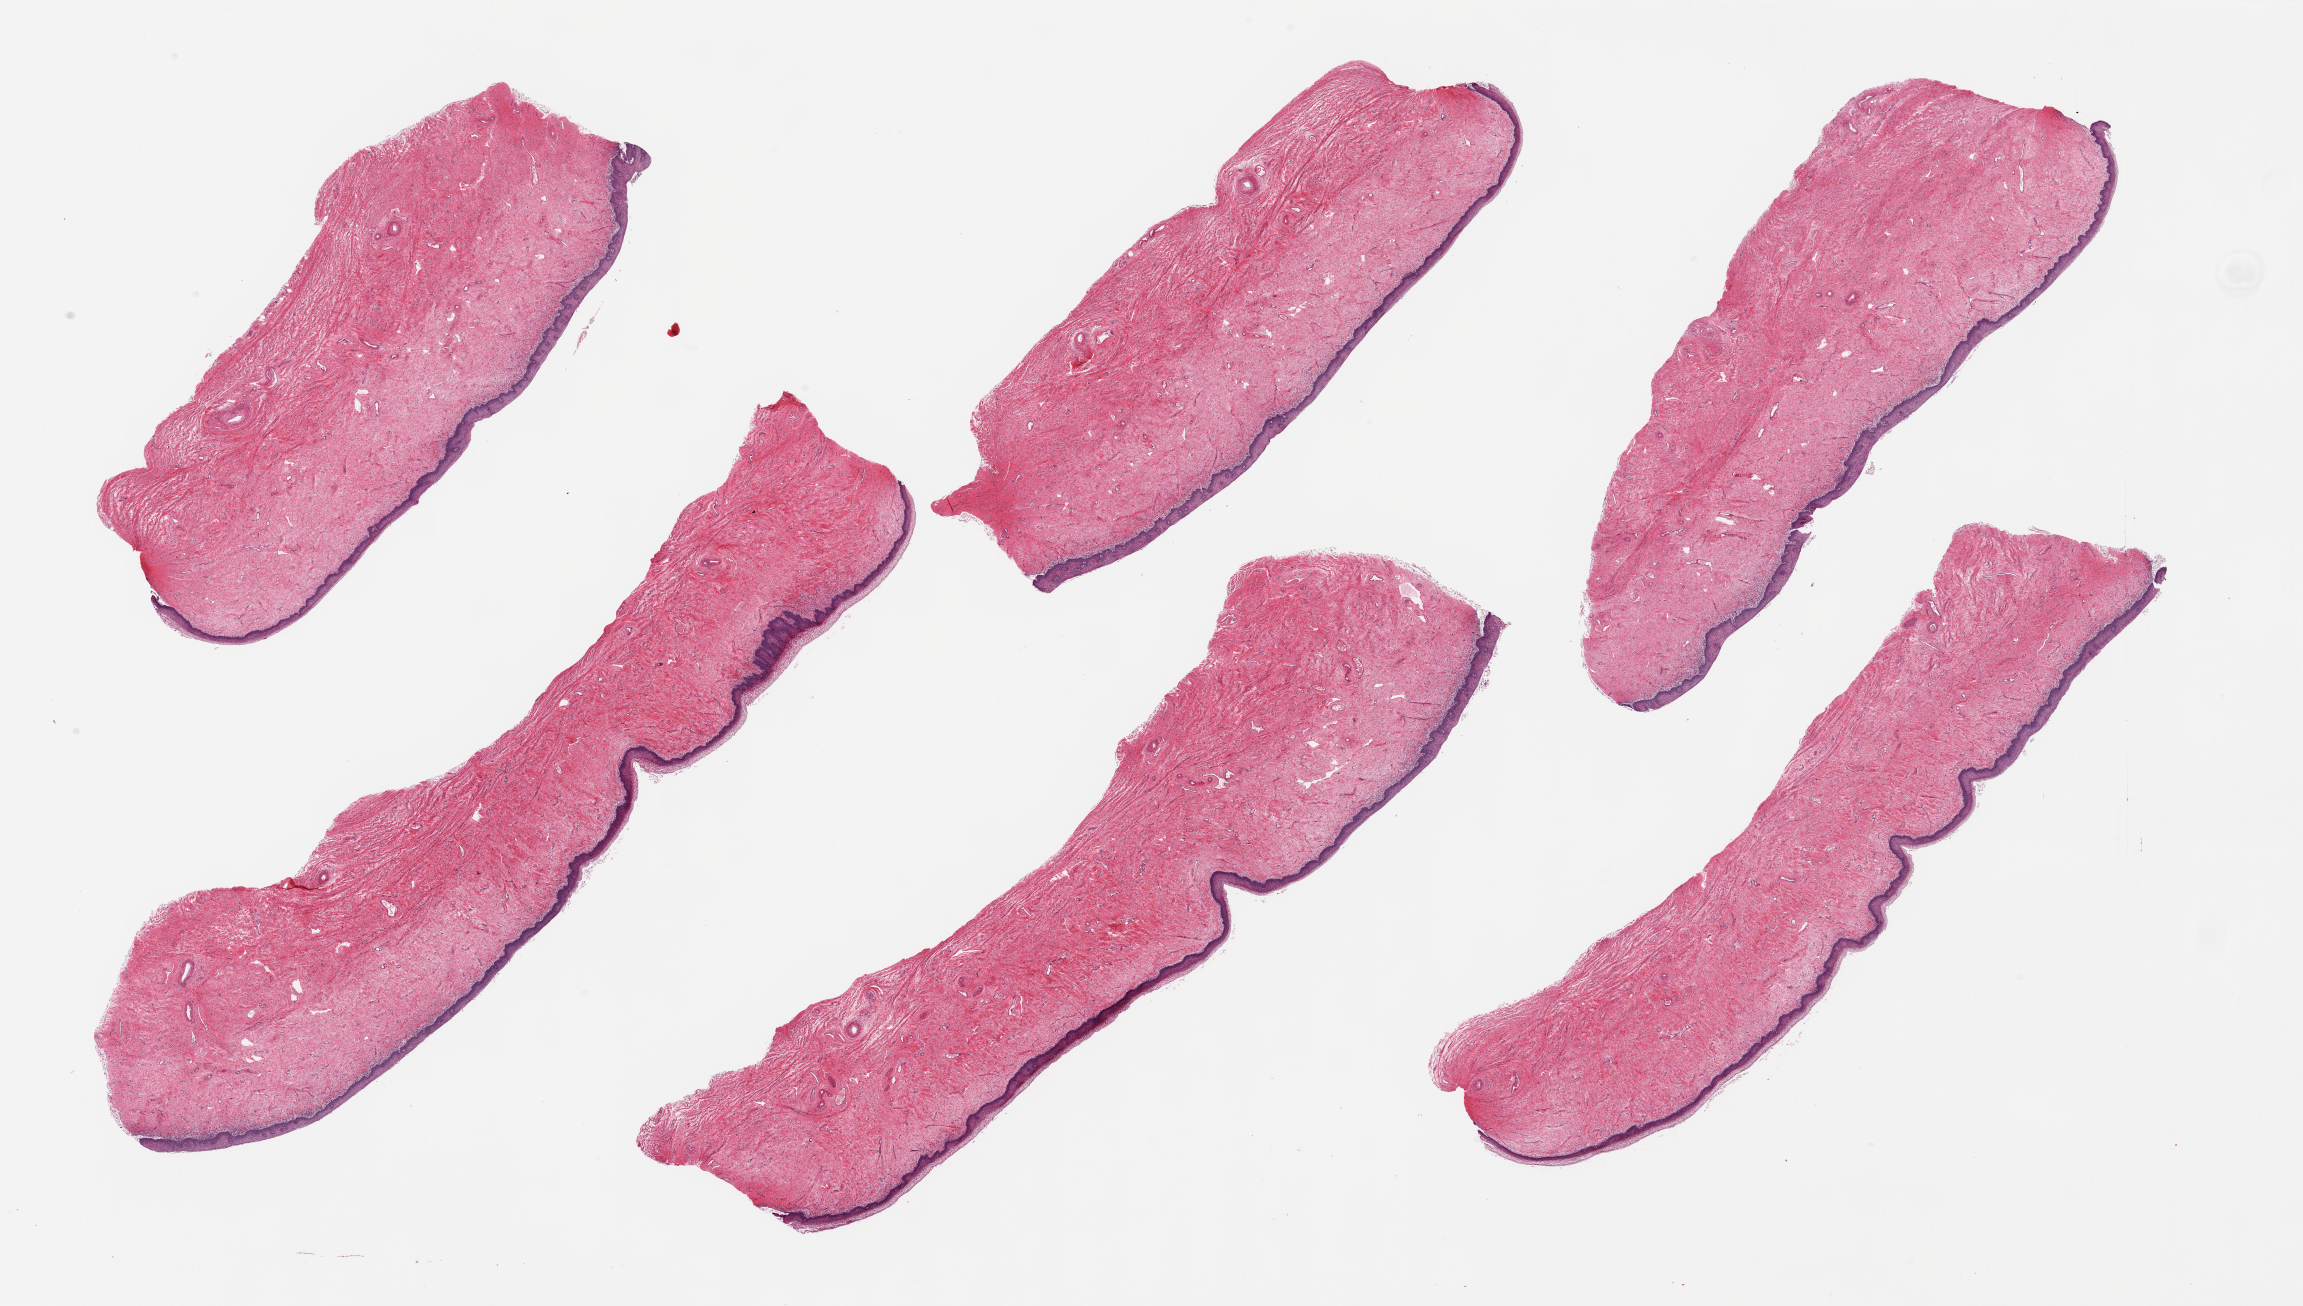
Whole-slide image, haematoxylin and eosin stain, shown as a low-resolution overview of the whole scanned area (about 36.4 x 20.7 mm); PAXgene-fixed, paraffin-embedded tissue; sampled site (target tissue): vagina; tissue donor sample. Donor: female.
Review note (as recorded): 6 pieces, Squamous mucosa is ~100 microns.